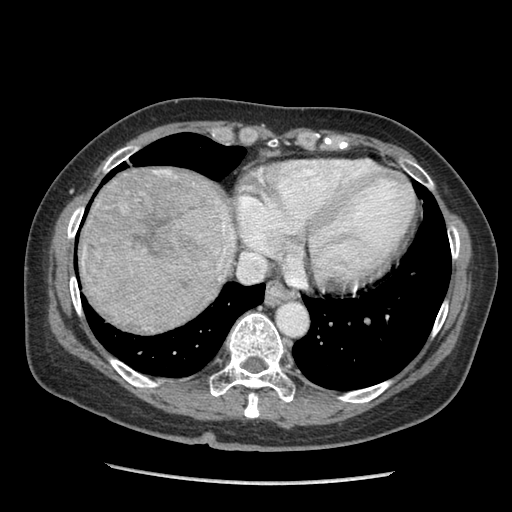
Contrast-enhanced abdominal CT (liver protocol), one axial slice. Position 85 of 105 along the scan axis. Reconstruction kernel STANDARD. Soft-tissue window (W 400 / L 40 HU). 512 × 512 image matrix, field of view 340 × 340 mm. From the clinical record (not read from this slice): diagnosis: hepatocellular carcinoma (patient treated with transarterial chemoembolisation; whether this scan precedes or follows treatment is not stated here); TNM stage (as recorded): Stage-I; Child-Pugh class: A; tumour size: 11.1 cm.
Structures marked on this image (semi-automatically segmented with operator editing):
- liver parenchyma outside the tumour (the mass and vessels are separate outlines, so this box may not span the whole liver): bounding box [x1, y1, x2, y2] px = [78, 168, 236, 318]
- mass: [80, 168, 236, 334]